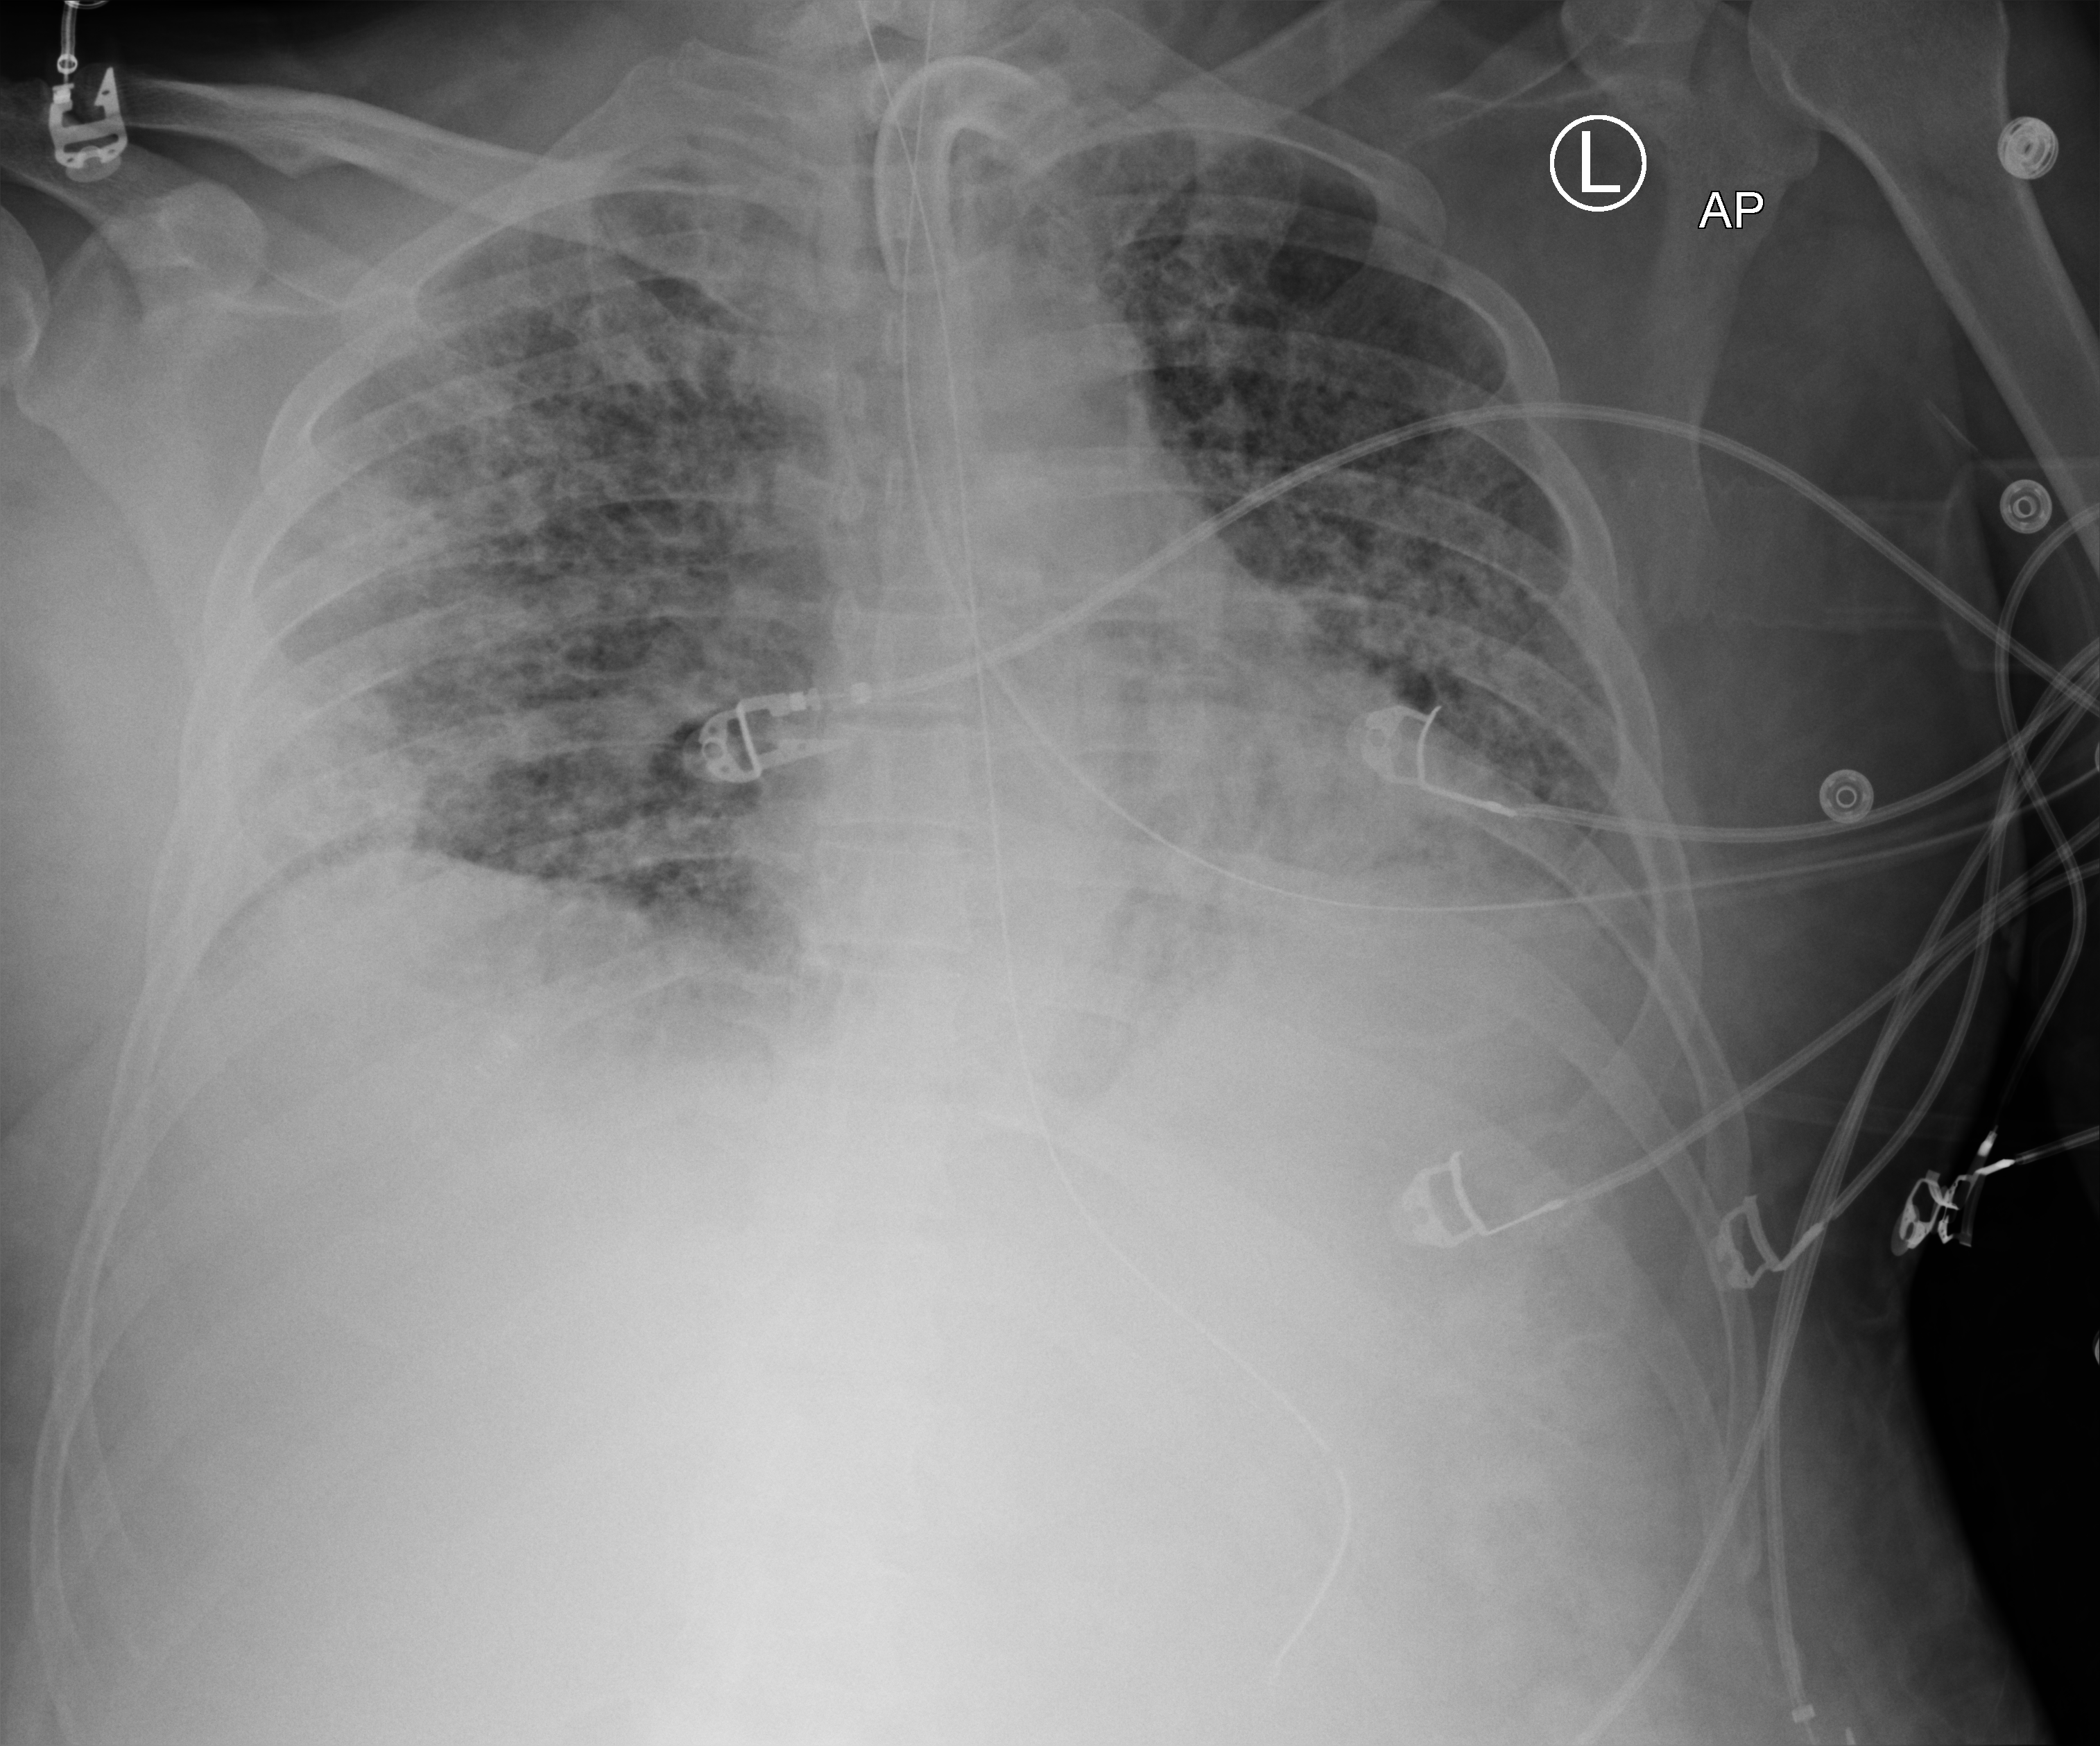
Bedside chest radiograph (computed radiography); anteroposterior (AP) projection. Male patient hospitalised with COVID-19, age 18–59 years.
From the hospital-stay record, not from the radiograph (when in the stay this image was taken is not recorded):
- mechanically ventilated during this hospital stay: yes
- length of hospital stay: 96 days